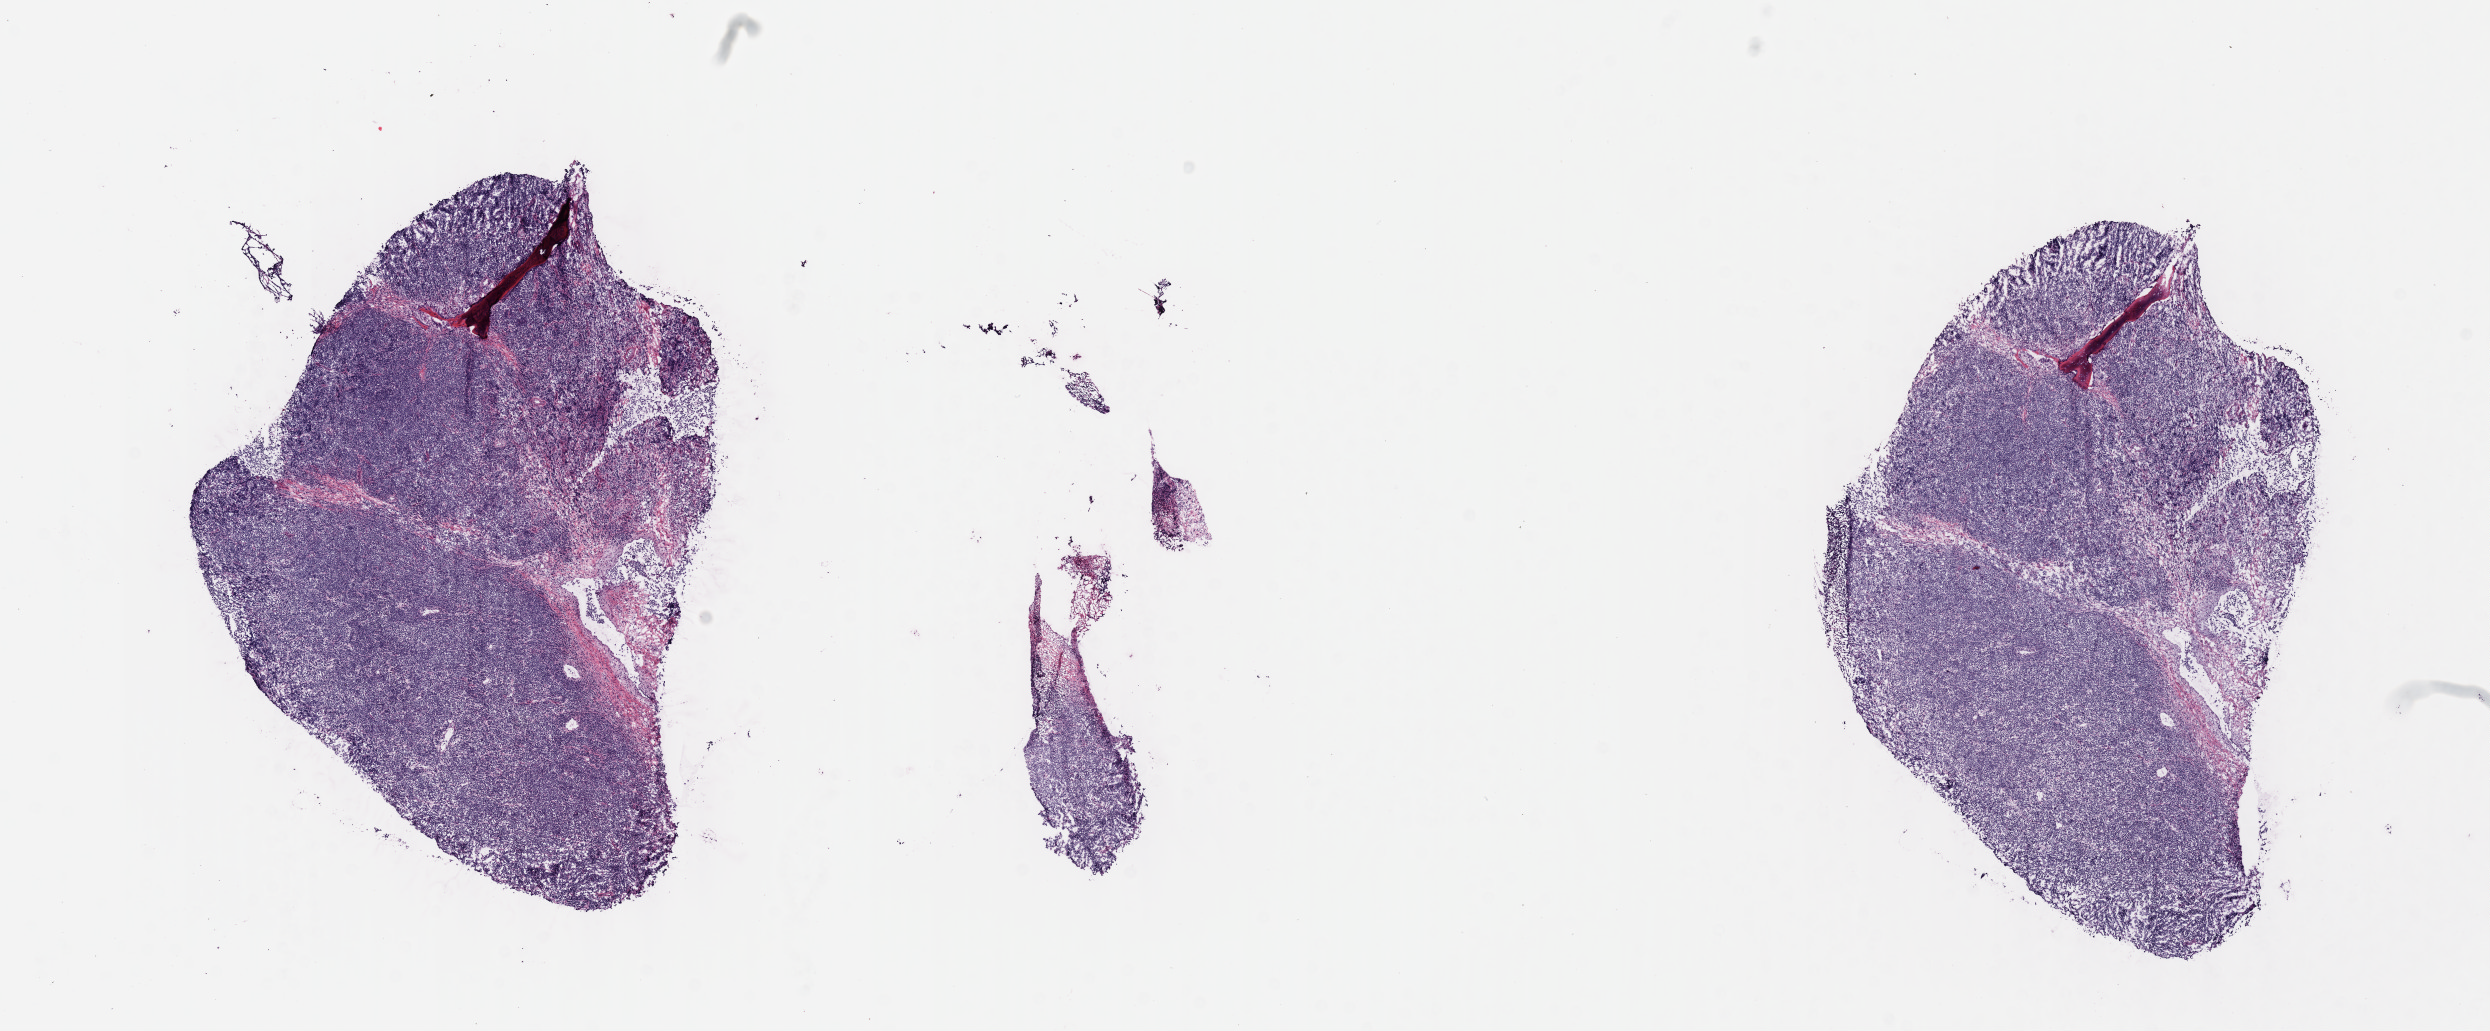
Whole-slide image, haematoxylin and eosin stain — low-resolution overview of the scanned area, about 20.1 x 8.3 mm; cryosection; specimen: primary tumor; site: cranium. Patient female; 11 years old. Pathologist review of this section (percent, as recorded): tumor cells 90%, tumor nuclei 90%, stromal cells 10%, necrosis 0%, normal cells 0%. Inflammatory infiltration, as recorded: lymphocyte infiltration 10%, monocyte infiltration 10%, neutrophil infiltration 5%.
Ann Arbor stage (patient): Stage I. Diagnosis: Burkitt lymphoma, NOS. Section: top of the tissue portion.